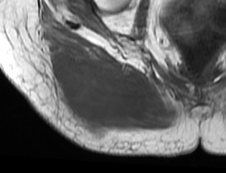
MRI of an extremity soft-tissue mass, one axial slice. Position 30 of 73 along the scan axis. MR volume resampled by the dataset authors to the PET/CT grid (not the native acquisition matrix). 3.27 mm slice thickness. 226 × 173 image matrix, field of view 221 × 169 mm. Female patient. Case-level facts recorded for this patient, not image findings: histological type: spindle cell suggestive of myxofibrosarcoma; grade: intermediate; site of the primary tumour: right buttock.
Annotated regions visible in this slice (expert contour drawn on MRI and transferred to this co-registered scan by the dataset authors):
- gross tumour volume (mass): box from (x=47, y=42) to (x=153, y=137) px